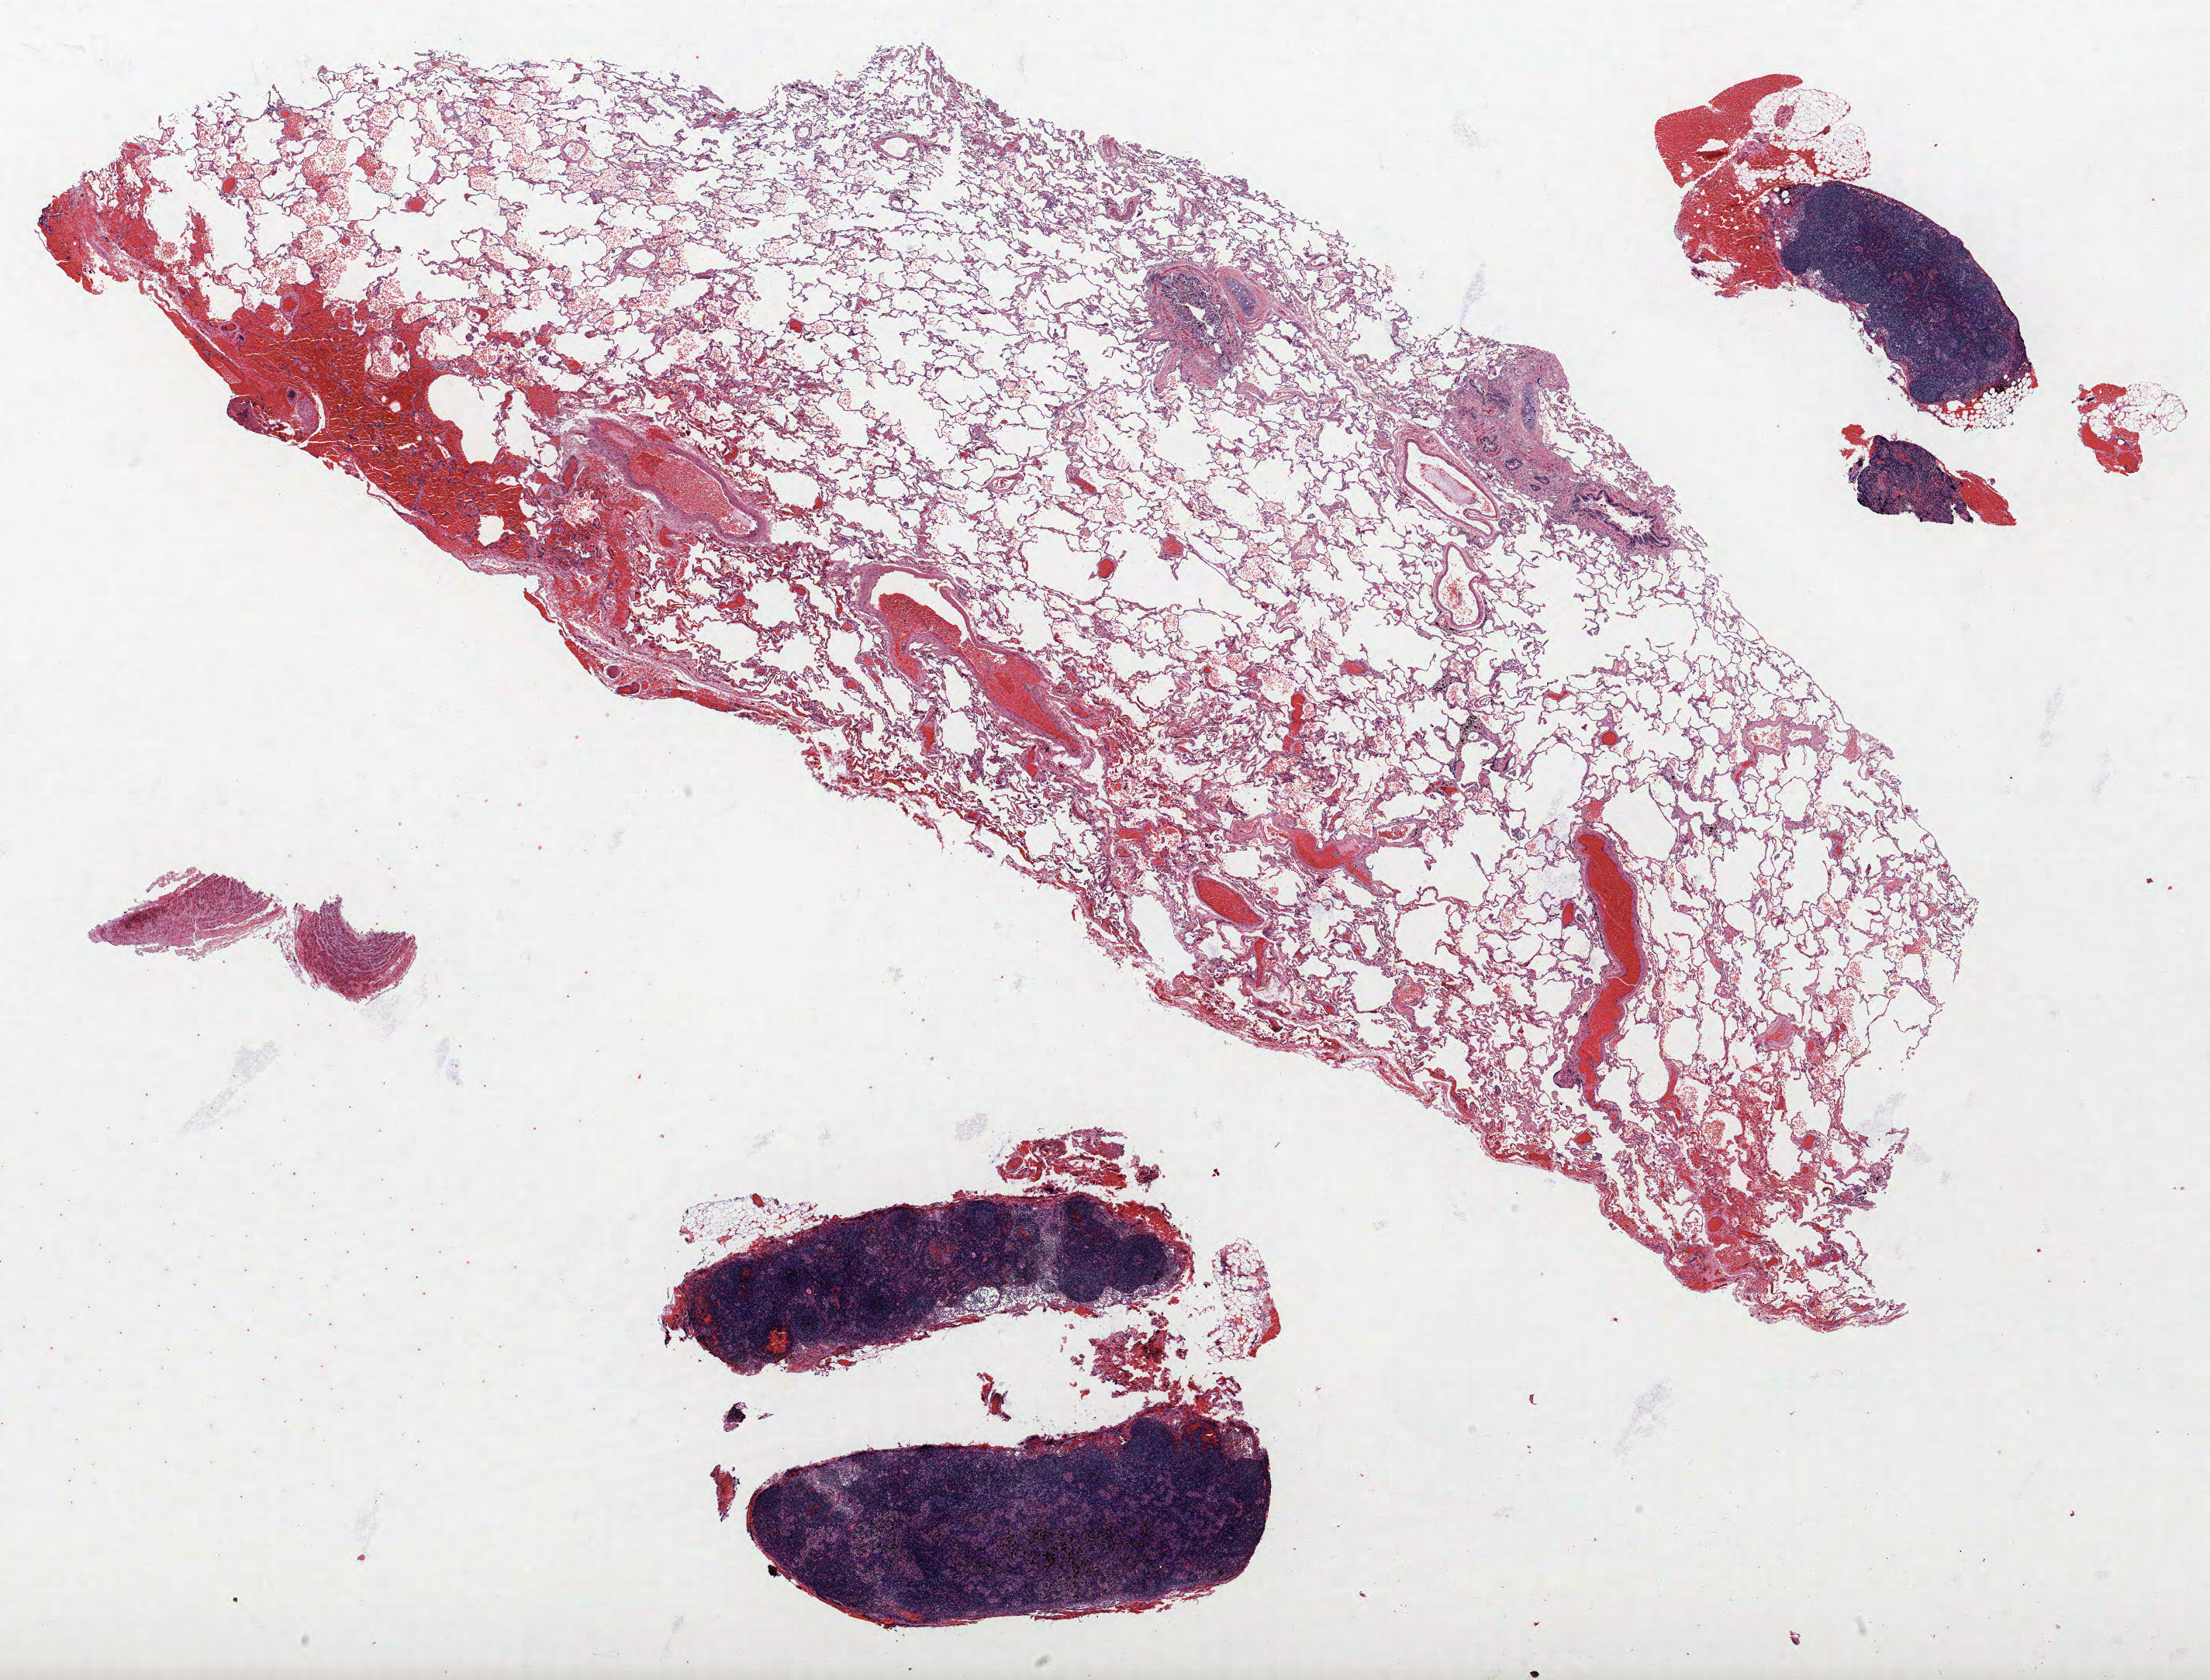
Whole-slide histology image, Hematoxylin and eosin (H&E) stained, shown as a low-resolution overview of the whole scanned area (about 22.8 x 17.3 mm, from a 40x scan), formalin-fixed paraffin-embedded (FFPE) section, lung. Male, age 62 at enrolment. Former smoker at enrolment. Grade: moderately differentiated (G2).
Tumour size (pathology): 7 mm. Primary tumour location (clinical record): right upper lobe. Stage (AJCC 6th edition): IA. Participant's lung-cancer diagnosis: Adenocarcinoma, NOS (ICD-O-3 8140/3).